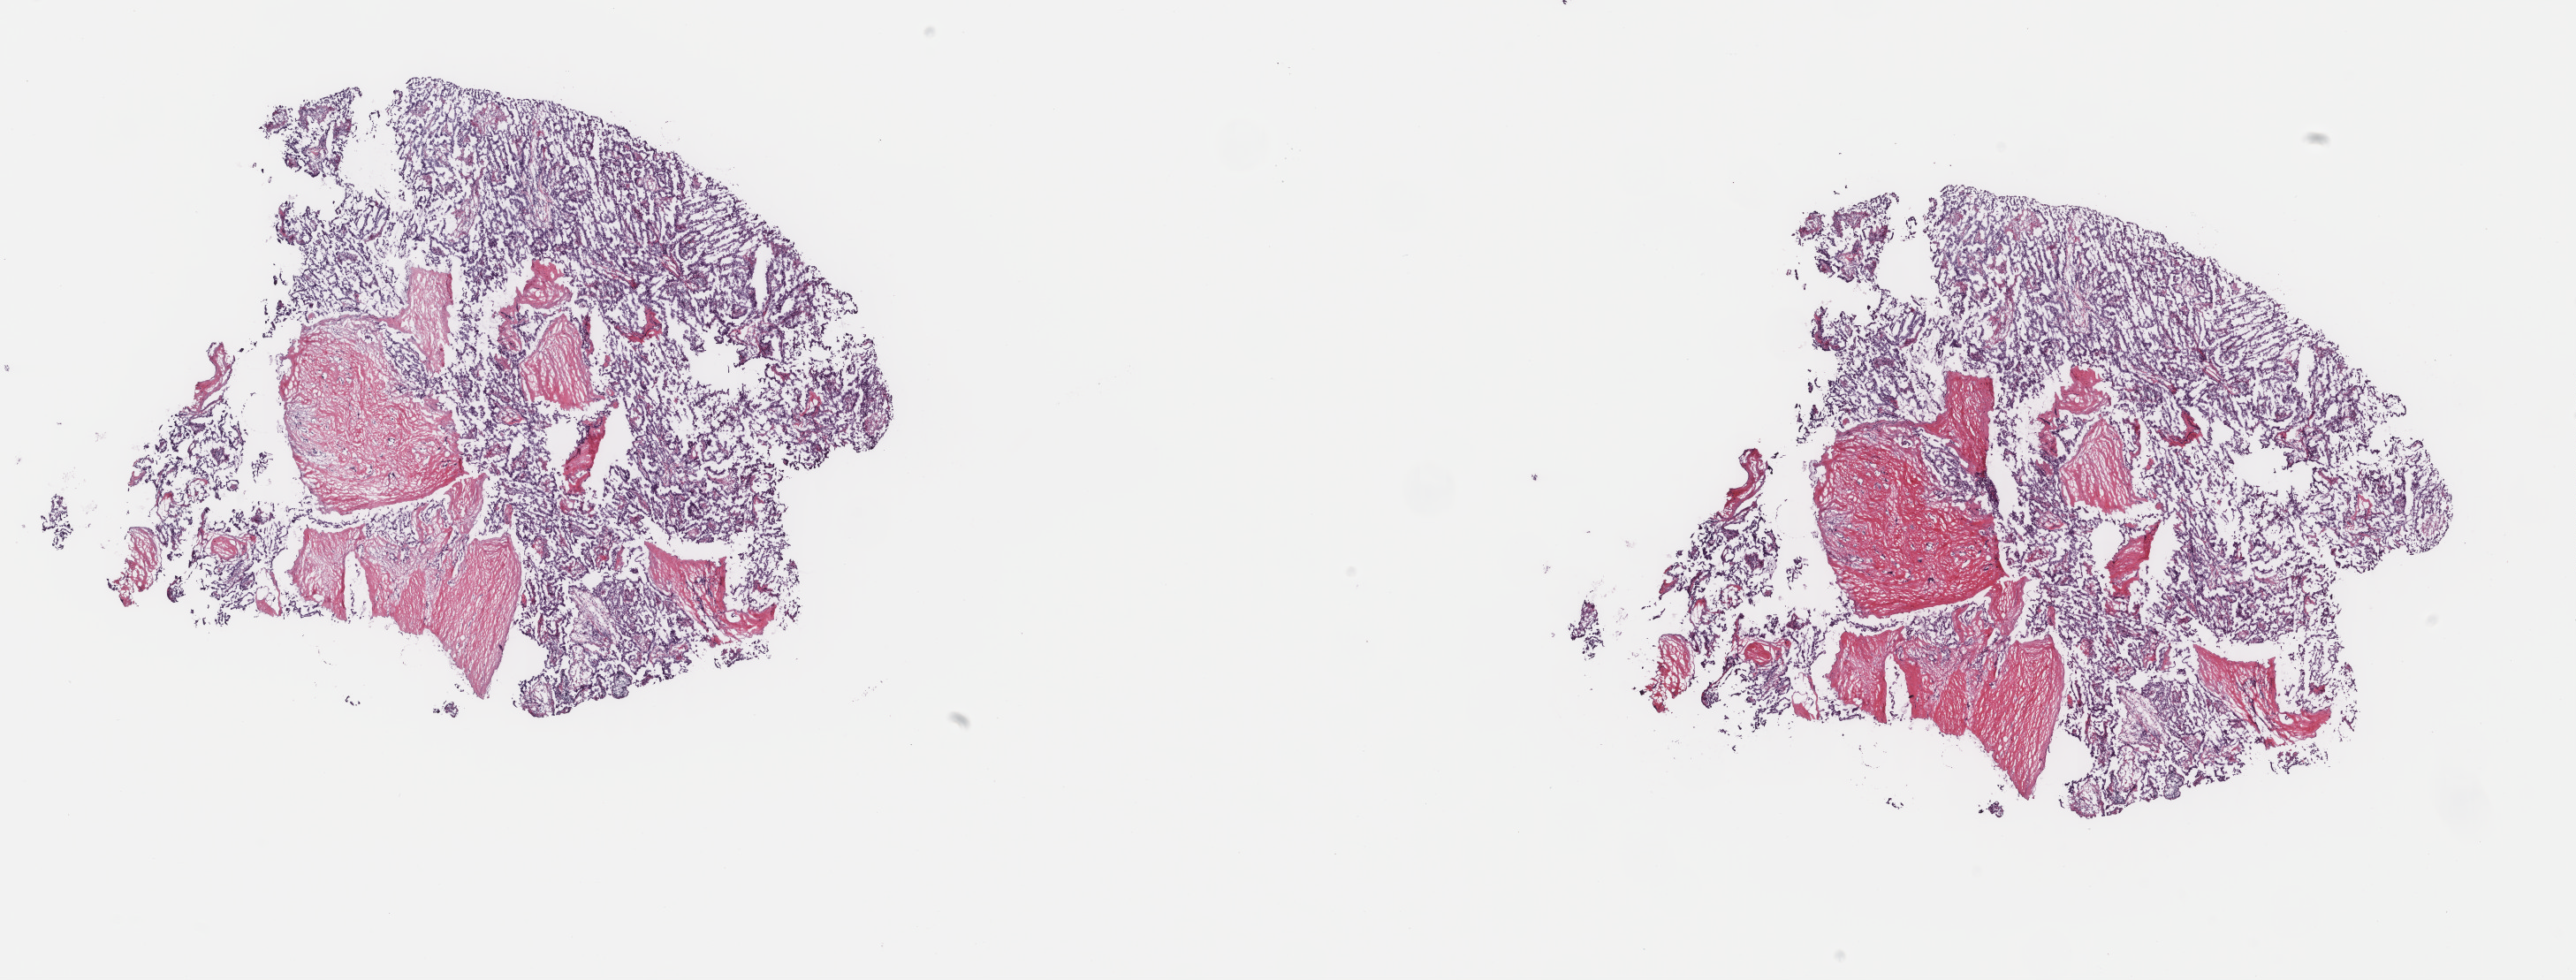
Digitized H&E-stained tissue section (whole slide), a low-resolution overview of the entire scanned area, about 23.1 x 8.8 mm; frozen section from the top of the tissue portion; sample: primary tumour, thyroid. Female patient; age at initial diagnosis 51 years. Composition of this section per pathologist review: tumour cells 60%, tumour nuclei 90%, normal cells 0%, stromal cells 40%, necrosis 0%. Inflammatory infiltration, as recorded: lymphocyte infiltration 1%, monocyte infiltration 1%, neutrophil infiltration 0%.
Lymph nodes positive (case pathology): 1 of 5 examined. Diagnosis: Papillary adenocarcinoma, NOS (thyroid gland). TNM: T3 N1b M0. AJCC pathologic stage: III (5th edition).